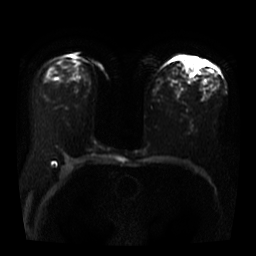
Breast MRI, one axial slice; slice 21 of 40 in the series (ordered by position); diffusion-weighted series; image 2 of 4 stored at this slice position (different b-values; order by instance number); 3 T; 5 mm slice thickness; 256 × 256 image matrix, field of view 360 × 360 mm. Female patient.
Outlined on this slice (outlined manually by an expert reader):
- tumour on diffusion-weighted imaging: bounding box [x1, y1, x2, y2] px = [183, 59, 200, 76]